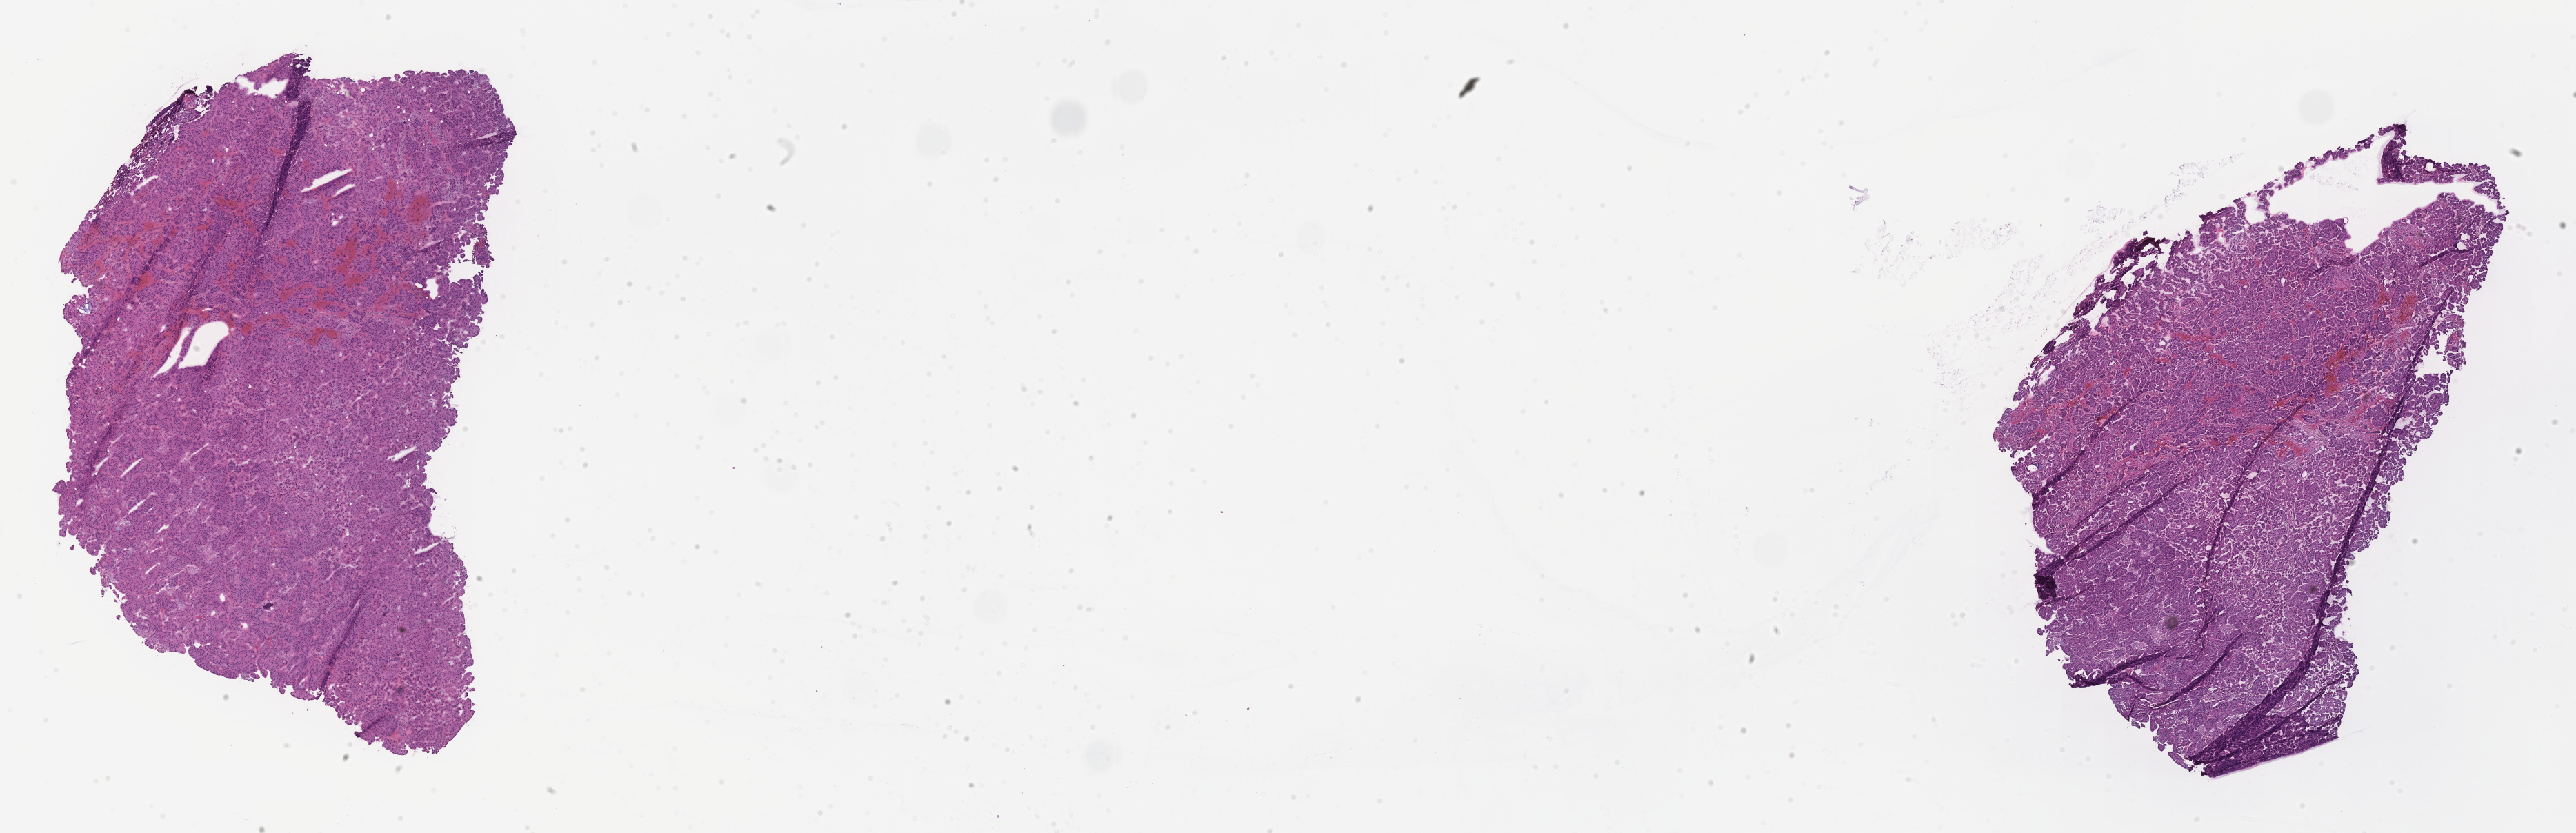
Digitized hematoxylin and eosin (H&E)-stained section — whole scanned area (about 30.1 x 9.7 mm) shown as a low-resolution overview, cryosection, specimen: primary tumor, site: breast. Female, age 69 years at initial diagnosis. Slide review estimates, as recorded: tumor cells 90%, tumor nuclei 90%, stromal cells 10%, necrosis 0%, normal cells 0%. Inflammatory infiltration, as recorded: lymphocyte infiltration 4%, monocyte infiltration 1%, neutrophil infiltration 2%.
Section: top of the tissue portion. Histologic diagnosis: Infiltrating duct carcinoma, NOS.